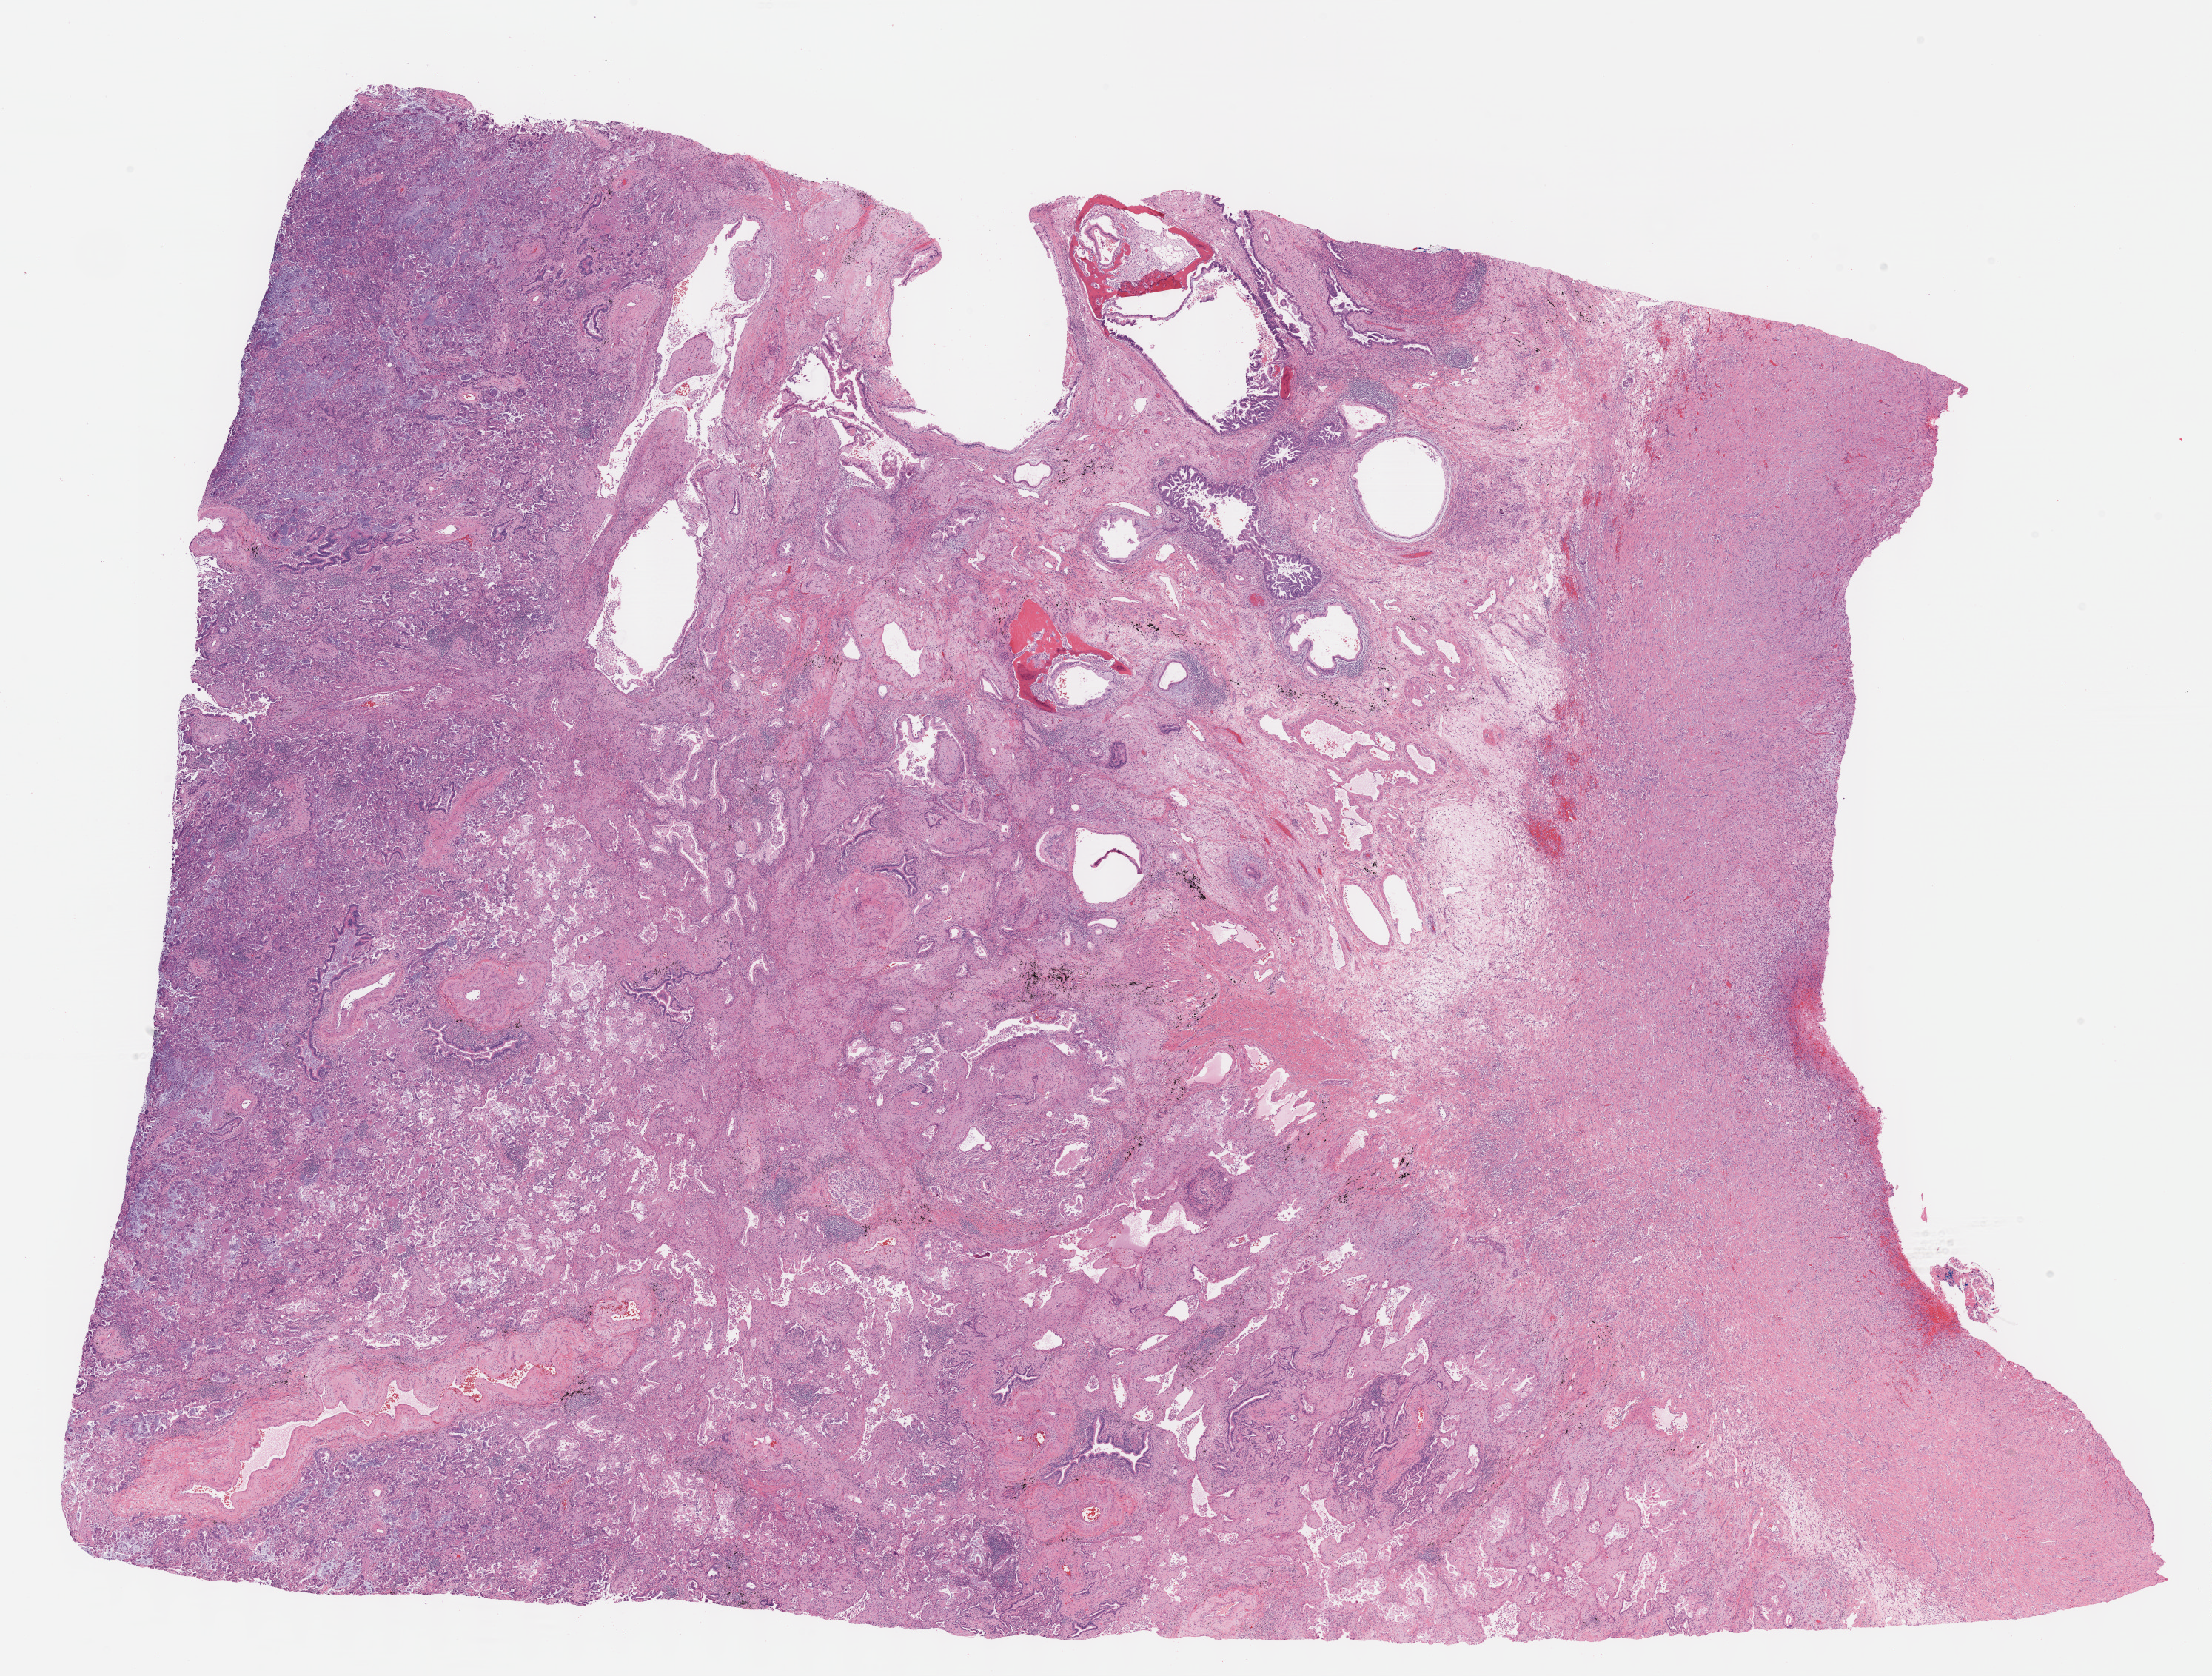
Digitized H&E tissue section (whole slide) — shown as a low-resolution overview of the whole scanned area (about 24.1 x 18.3 mm). Formalin-fixed paraffin-embedded (FFPE) diagnostic section. Lung, primary tumour sample. Patient: male, age at initial diagnosis 77 years.
• histologic diagnosis: Mucinous adenocarcinoma
• AJCC pathologic stage: IIB